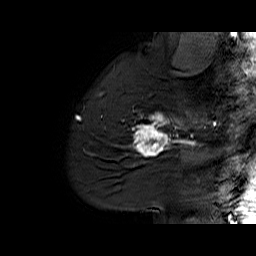
Breast MRI (dynamic contrast-enhanced), one sagittal slice. Slice 48 of 60 in the series (ordered by position). Dynamic contrast-enhanced series, time point 2 of 6 at this slice position (early post-contrast). 1.5 T. TE 6.1 ms, TR 32.9 ms. 4 mm slice thickness. 256 × 256 image matrix. Female patient. Case-level facts recorded for this patient, not image findings: setting: breast cancer imaged before/during neoadjuvant chemotherapy; receptor status: HER2-positive.
Annotated regions visible in this slice (semi-automatic segmentation, software-assisted and operator-edited):
- analysis volume of interest (the breast-tissue region the enhancement analysis was run in; not a lesion): bounding box <127,95,194,165> (left, top, right, bottom; pixels)
- tumour enhancement mask (voxels above the 100 % enhancement threshold inside the analysis volume of interest): <131,112,194,156>